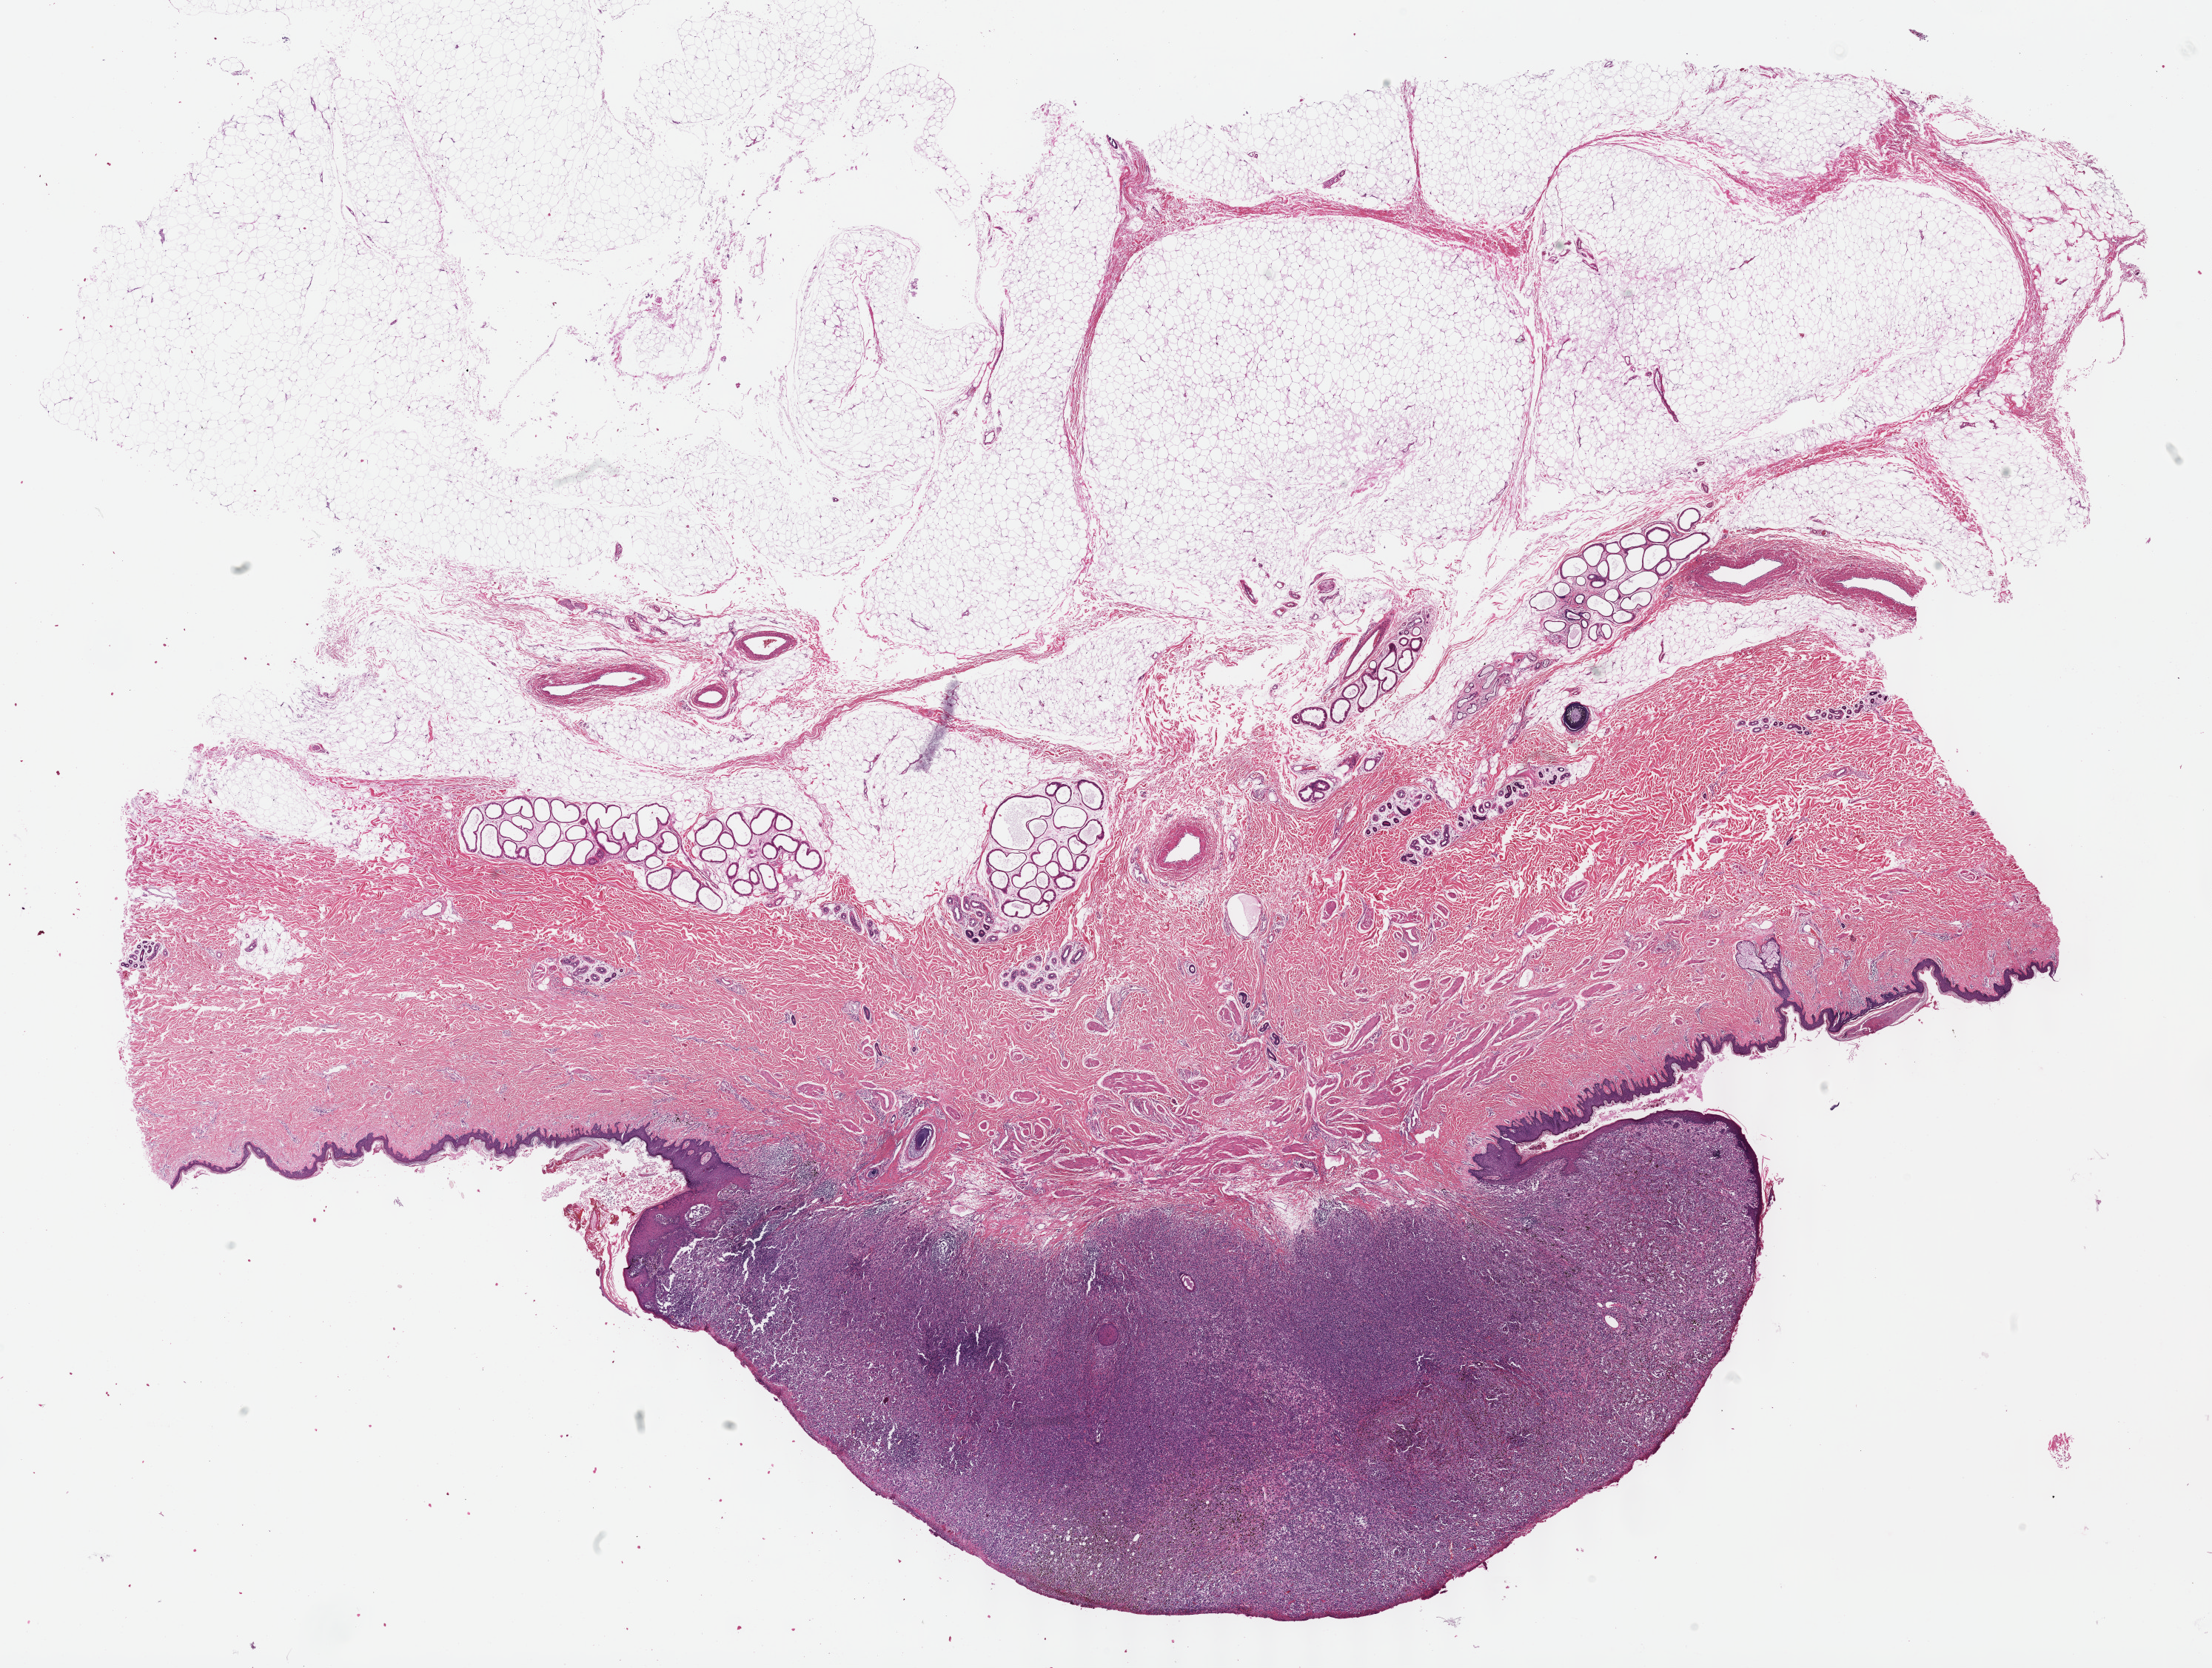
Hematoxylin and eosin (H&E) stained whole-slide image — shown as a low-resolution overview of the whole scanned area (about 24.1 x 18.2 mm). Formalin-fixed paraffin-embedded (FFPE) diagnostic section. Skin, primary tumour sample. Male, age 63 years at initial diagnosis.
AJCC pathologic stage: IIC (7th edition). TNM: T4b N0 M0. Pathologic diagnosis: Malignant melanoma, NOS.